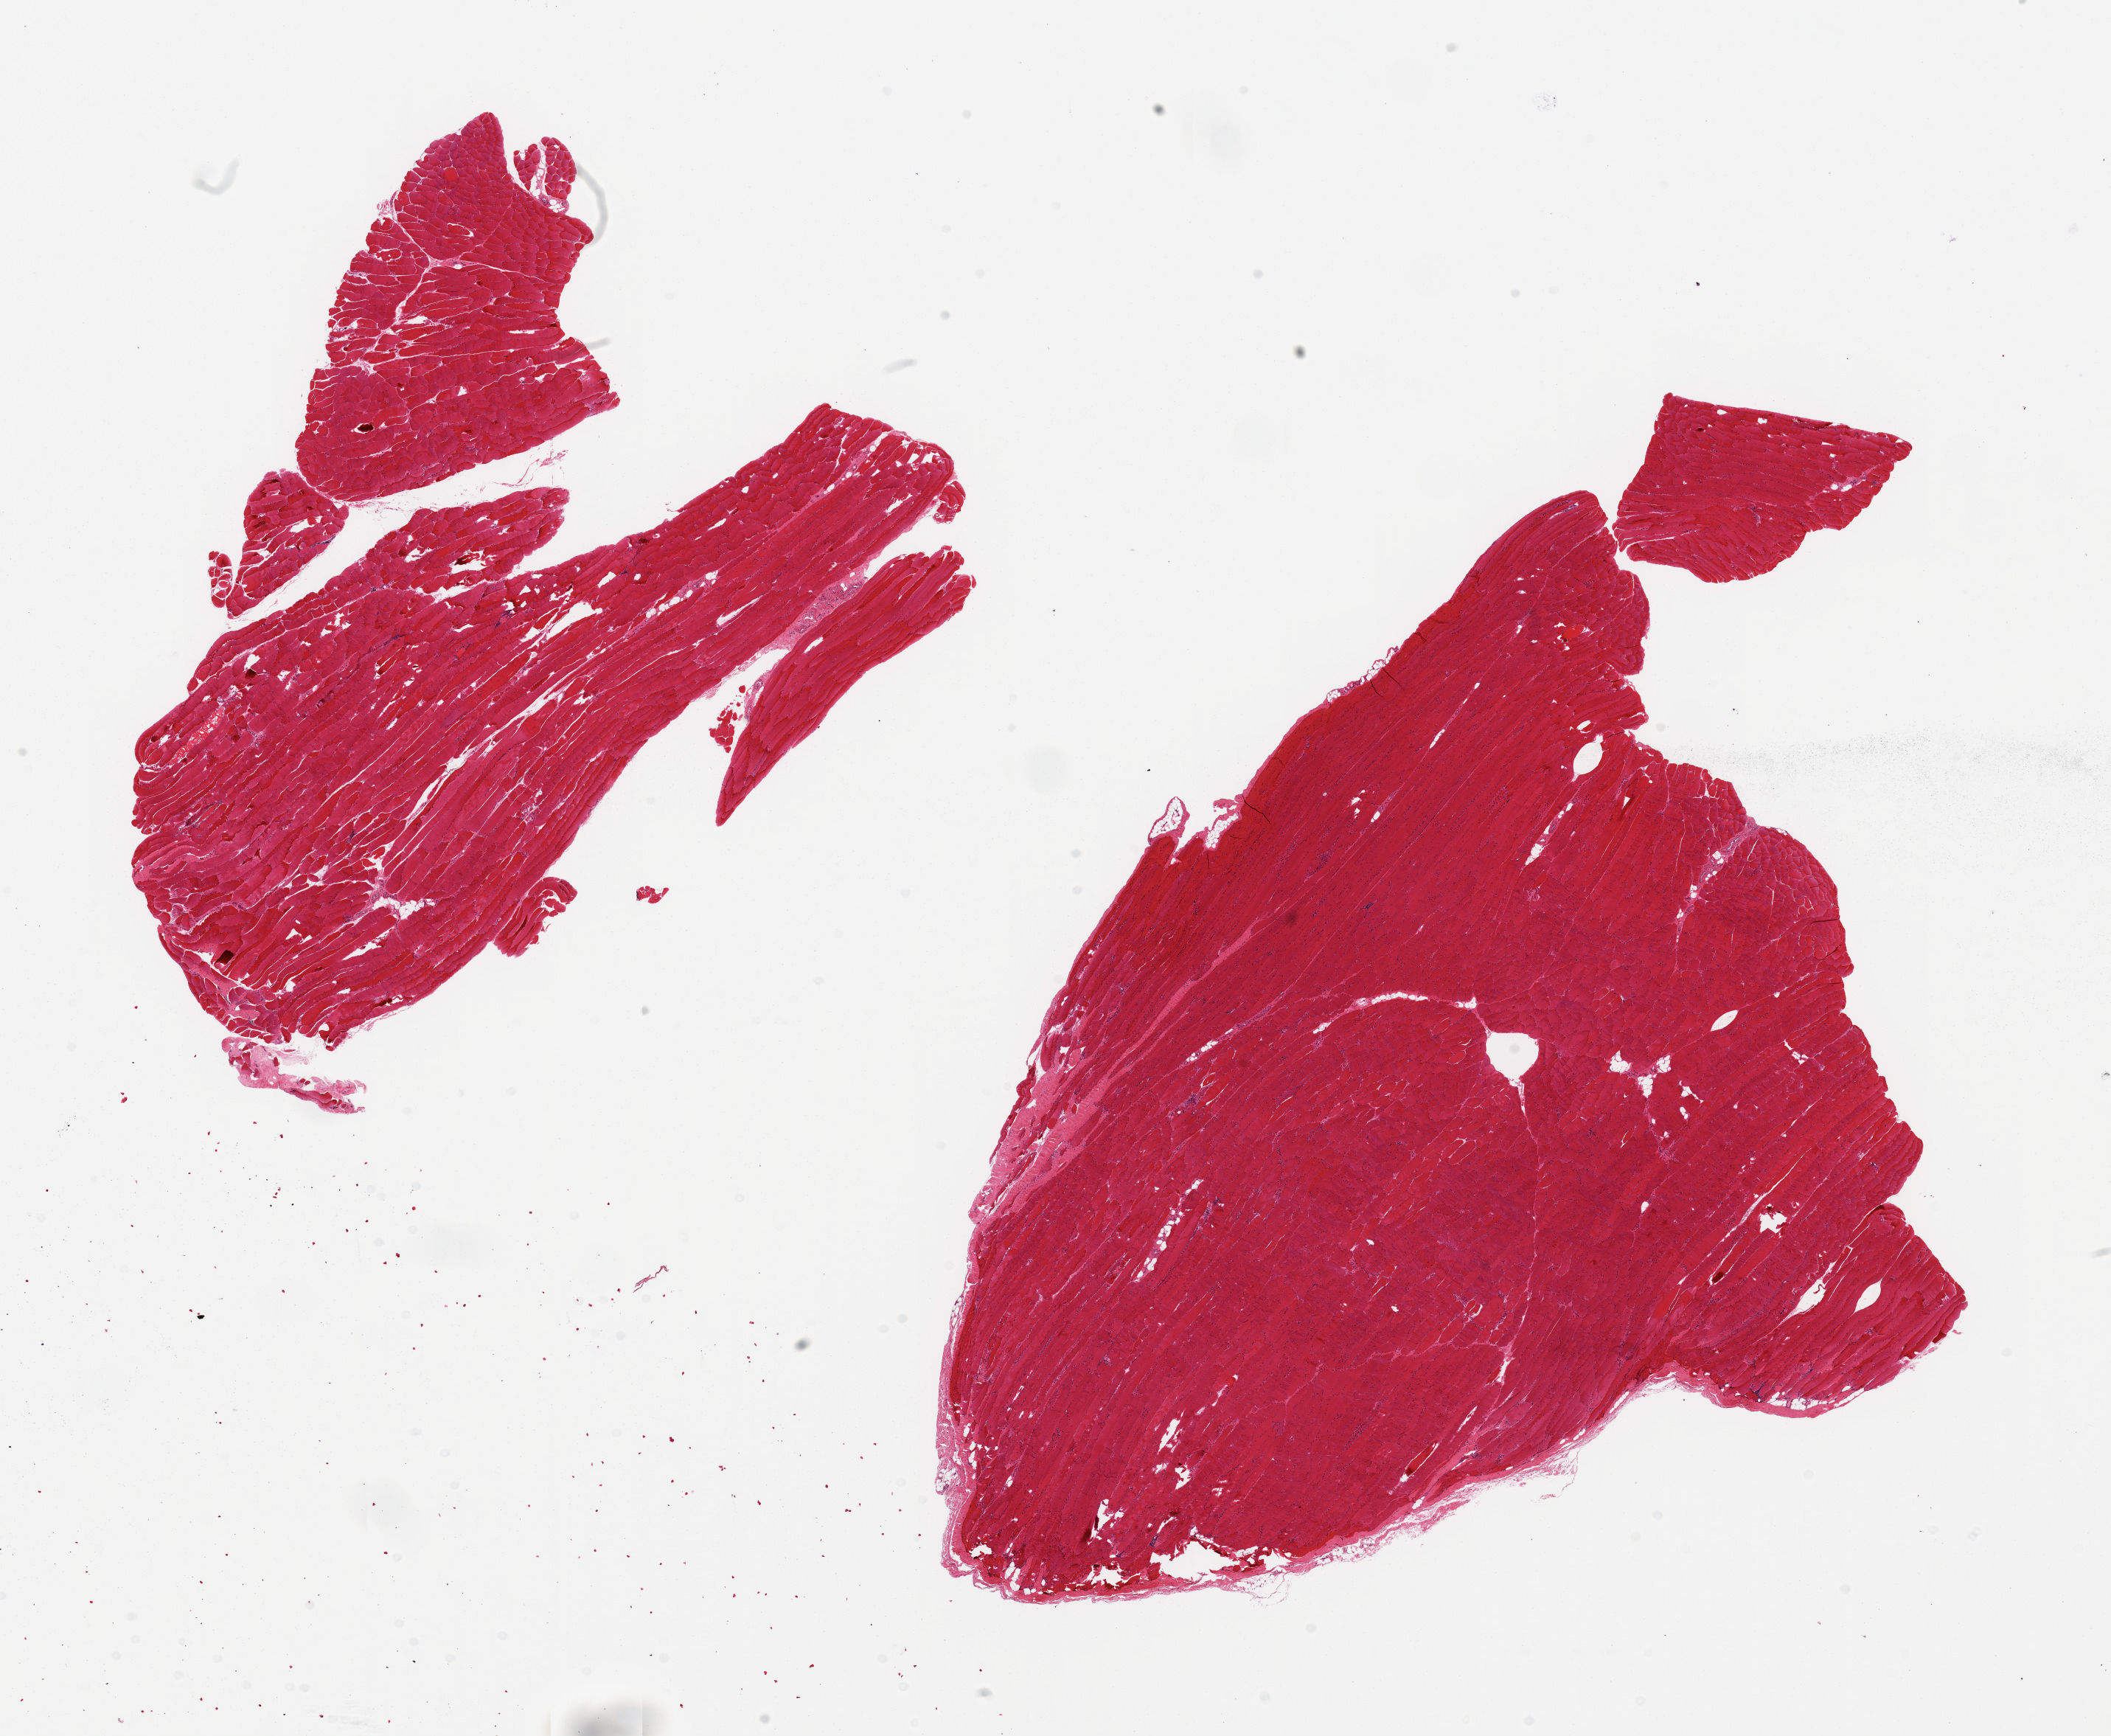
Digitized haematoxylin and eosin-stained section, a low-resolution overview of the entire scanned area, about 22.6 x 18.6 mm, PAXgene-fixed paraffin-embedded (PFPE) section, sampled site (target tissue): skeletal muscle, donor tissue sample. Male donor.
Pathologist's review note for this sample: 2 pieces ~11x8mm. Minimal interstitial fat.